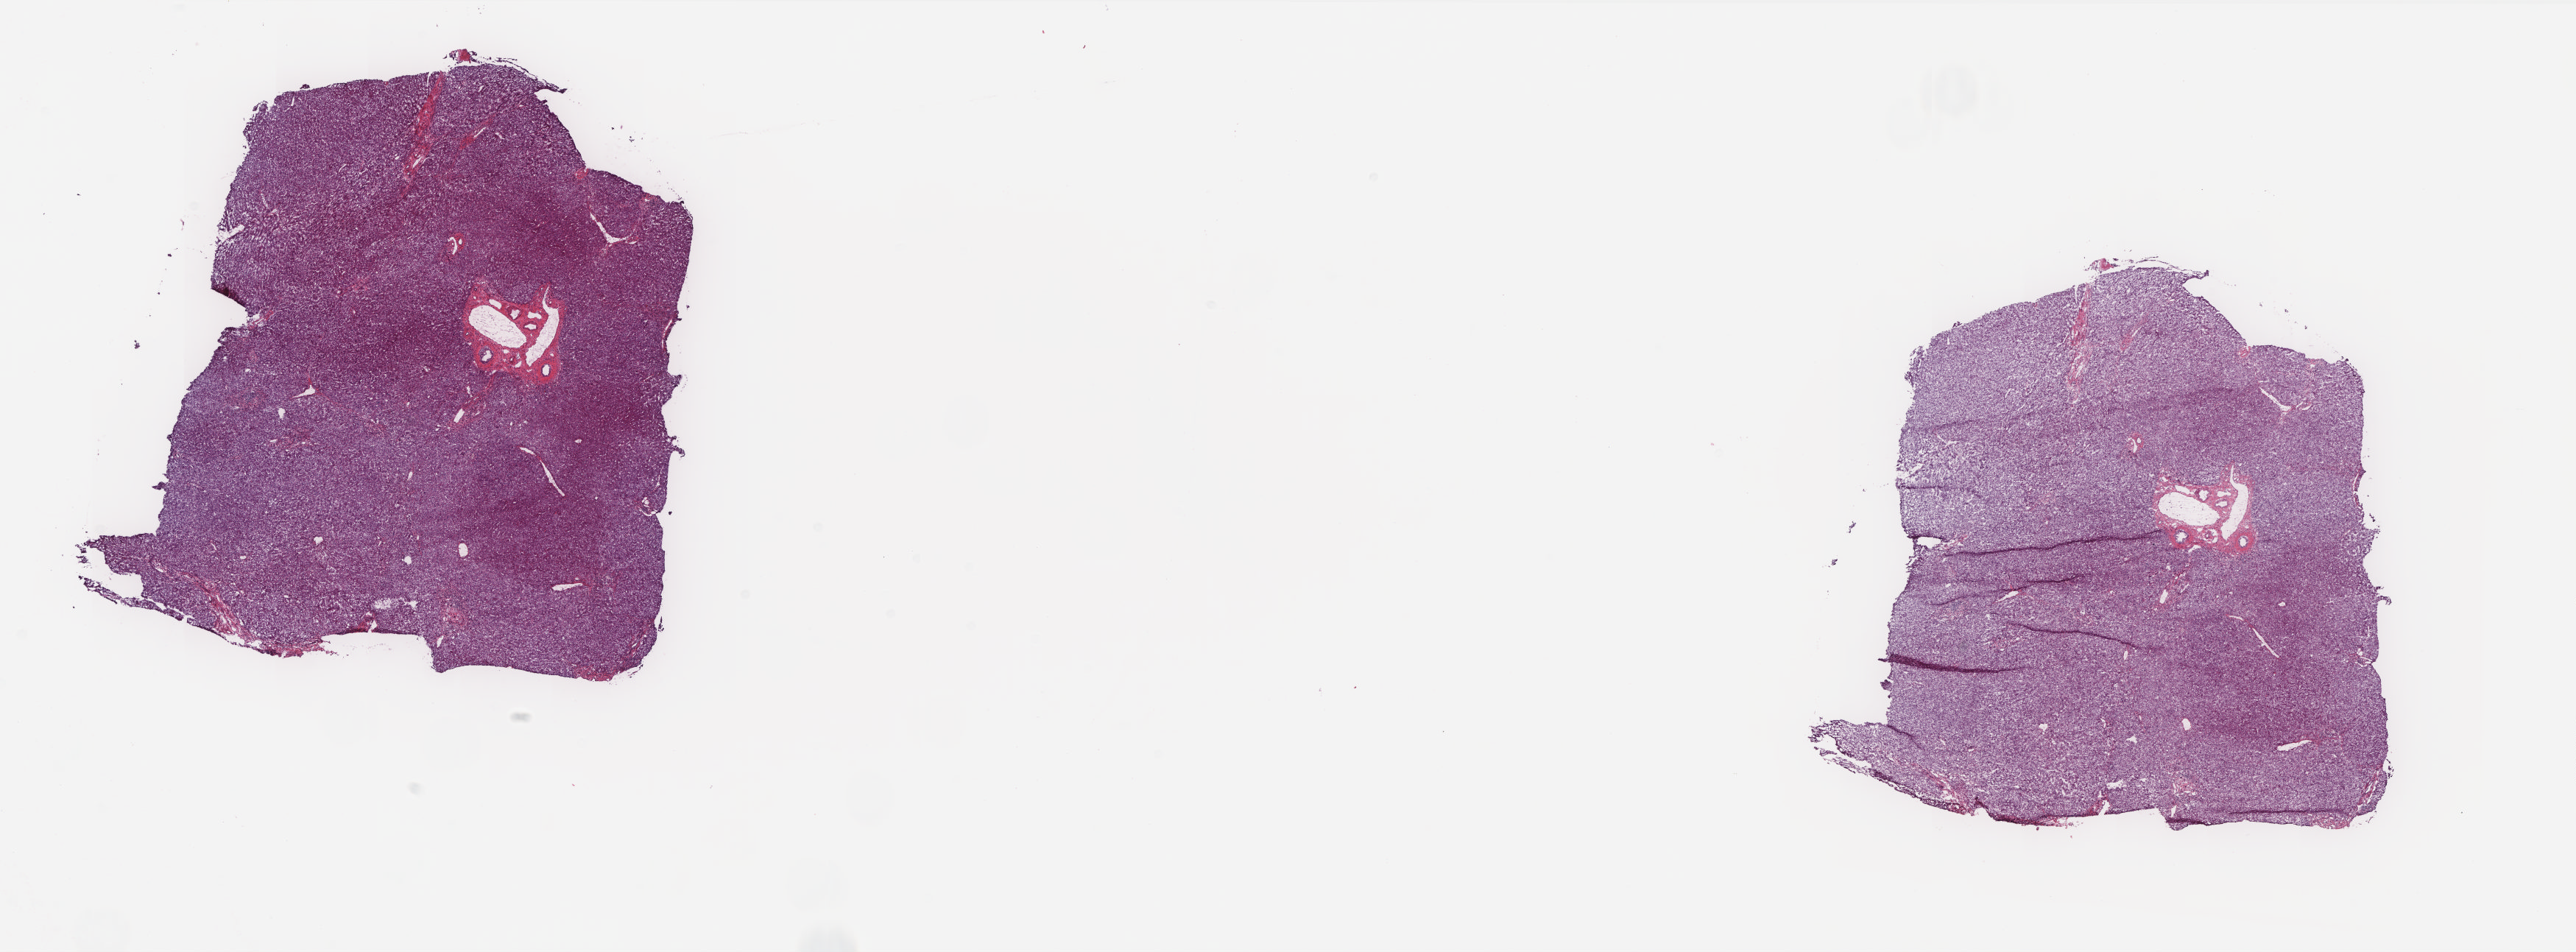
Digitized Hematoxylin and eosin (H&E) stained tissue section (whole slide) — low-resolution overview of the scanned area, about 27.9 x 10.3 mm (acquisition: 20x scan). Frozen section from the top of the tissue portion. Sample: solid tissue normal (non-tumour tissue), liver. Male, age 70 years at initial diagnosis. Pathologist review of this section (percent, as recorded): tumour cells 0%, tumour nuclei 0%.
This section: solid tissue normal sample (biorepository sample class). Patient diagnosis: Hepatocellular carcinoma, NOS.